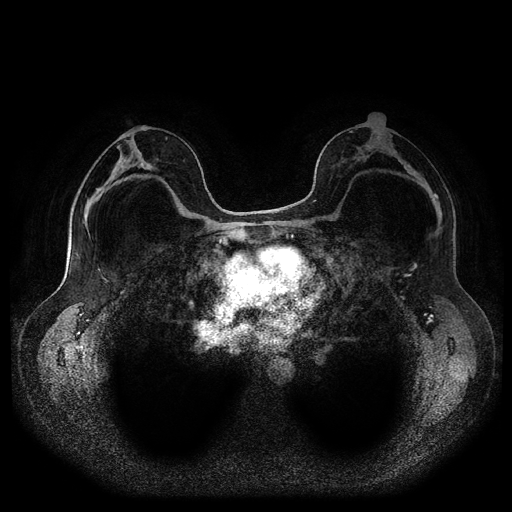
Breast MRI (dynamic contrast-enhanced, multi-phase), one axial slice; position 56 of 116 along the scan axis; dynamic contrast-enhanced series, time point 2 of 5 at this slice position (early post-contrast); 1.5 T; TE 2.6 ms, TR 5.3 ms; 2.2 mm slice thickness; 512 × 512 image matrix, field of view 360 × 360 mm. Patient: female, 46 years.
Outlined on this slice (semi-automatic segmentation, software-assisted and operator-edited):
- breast lesion (labelled 'tumour' in the annotation; benign lesions carry a separate 'benign' label): bounding box [x1, y1, x2, y2] px = [116, 144, 121, 150]